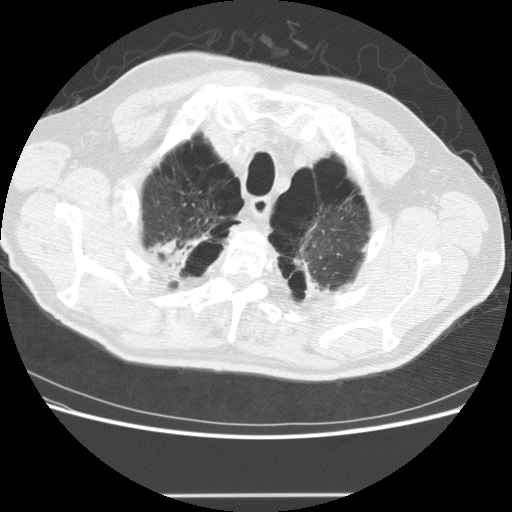
Axial slice from a low-dose chest CT screening exam, third screening round (two years after baseline), lung window (W 1500 / L -600 HU), 2.5 mm slice thickness, slice 27 of 151 in the series, 512 × 512 image matrix. Male, age 68 years at enrolment. Former smoker at enrolment.
Expert-annotated lung lesion, box from (x=131, y=214) to (x=216, y=288) px. The screening reader recorded 2 non-calcified nodules or masses ≥4 mm on this exam (lingula, left lower lobe); which of them this box marks is not recorded.